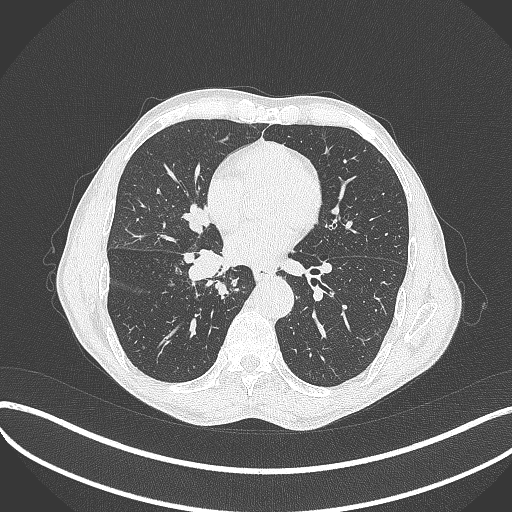
Chest CT, one axial slice. Position 196 of 481 along the scan axis. 120 kVp. Lung window (W 1500 / L -600 HU). 1 mm slice thickness. 512 × 512 image matrix, field of view 400 × 400 mm. Patient: male, 65 years. From the clinical record (not read from this slice): clinical TNM (as recorded): T2a N0 M0; histopathological grade: G2.
Outlined on this slice (bounding box drawn by a radiologist):
- lung tumour (recorded histology: squamous cell carcinoma): box from (x=180, y=245) to (x=240, y=302) px